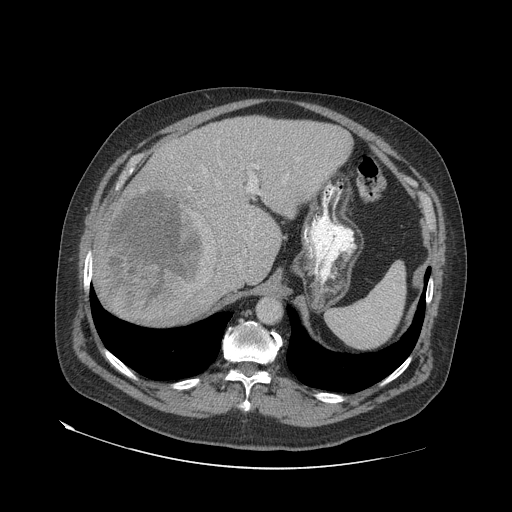
Contrast-enhanced abdominal CT (liver protocol), one axial slice. Position 50 of 79 along the scan axis. 140 kVp. Soft-tissue window (W 400 / L 40 HU). 2.5 mm slice thickness. 512 × 512 image matrix. From the clinical record (not read from this slice): diagnosis: hepatocellular carcinoma (patient treated with transarterial chemoembolisation; whether this scan precedes or follows treatment is not stated here); TNM stage (as recorded): Stage-IVA; Child-Pugh class: A; tumour differentiation: well differentiated.
Annotated regions visible in this slice (semi-automatic segmentation, software-assisted and operator-edited):
- liver parenchyma outside the tumour (the mass and vessels are separate outlines, so this box may not span the whole liver): bounding box [x1, y1, x2, y2] px = [94, 116, 350, 322]
- mass: [100, 191, 219, 325]
- liver vessels: [188, 166, 258, 190]